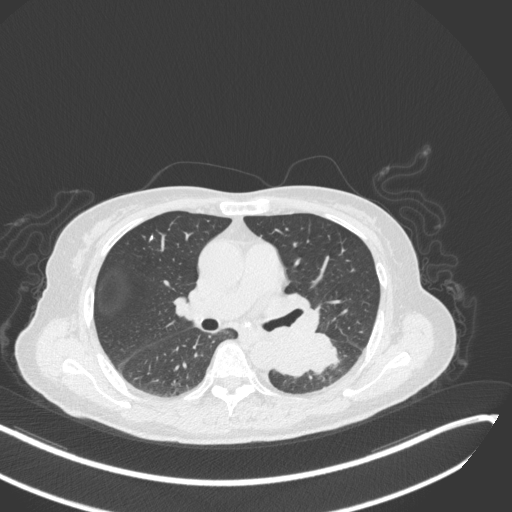
Chest CT, one axial slice; 120 kVp; lung window (W 1500 / L -600 HU); 1 mm slice thickness; 512 × 512 image matrix, field of view 400 × 400 mm. Patient: female, 64 years. From the clinical record (not read from this slice): clinical TNM (as recorded): T3 N1 M1.
Structures marked on this image (rectangle marked by the reading radiologist):
- lung tumour (recorded histology: small cell carcinoma): bounding box [x1, y1, x2, y2] px = [271, 331, 343, 380]